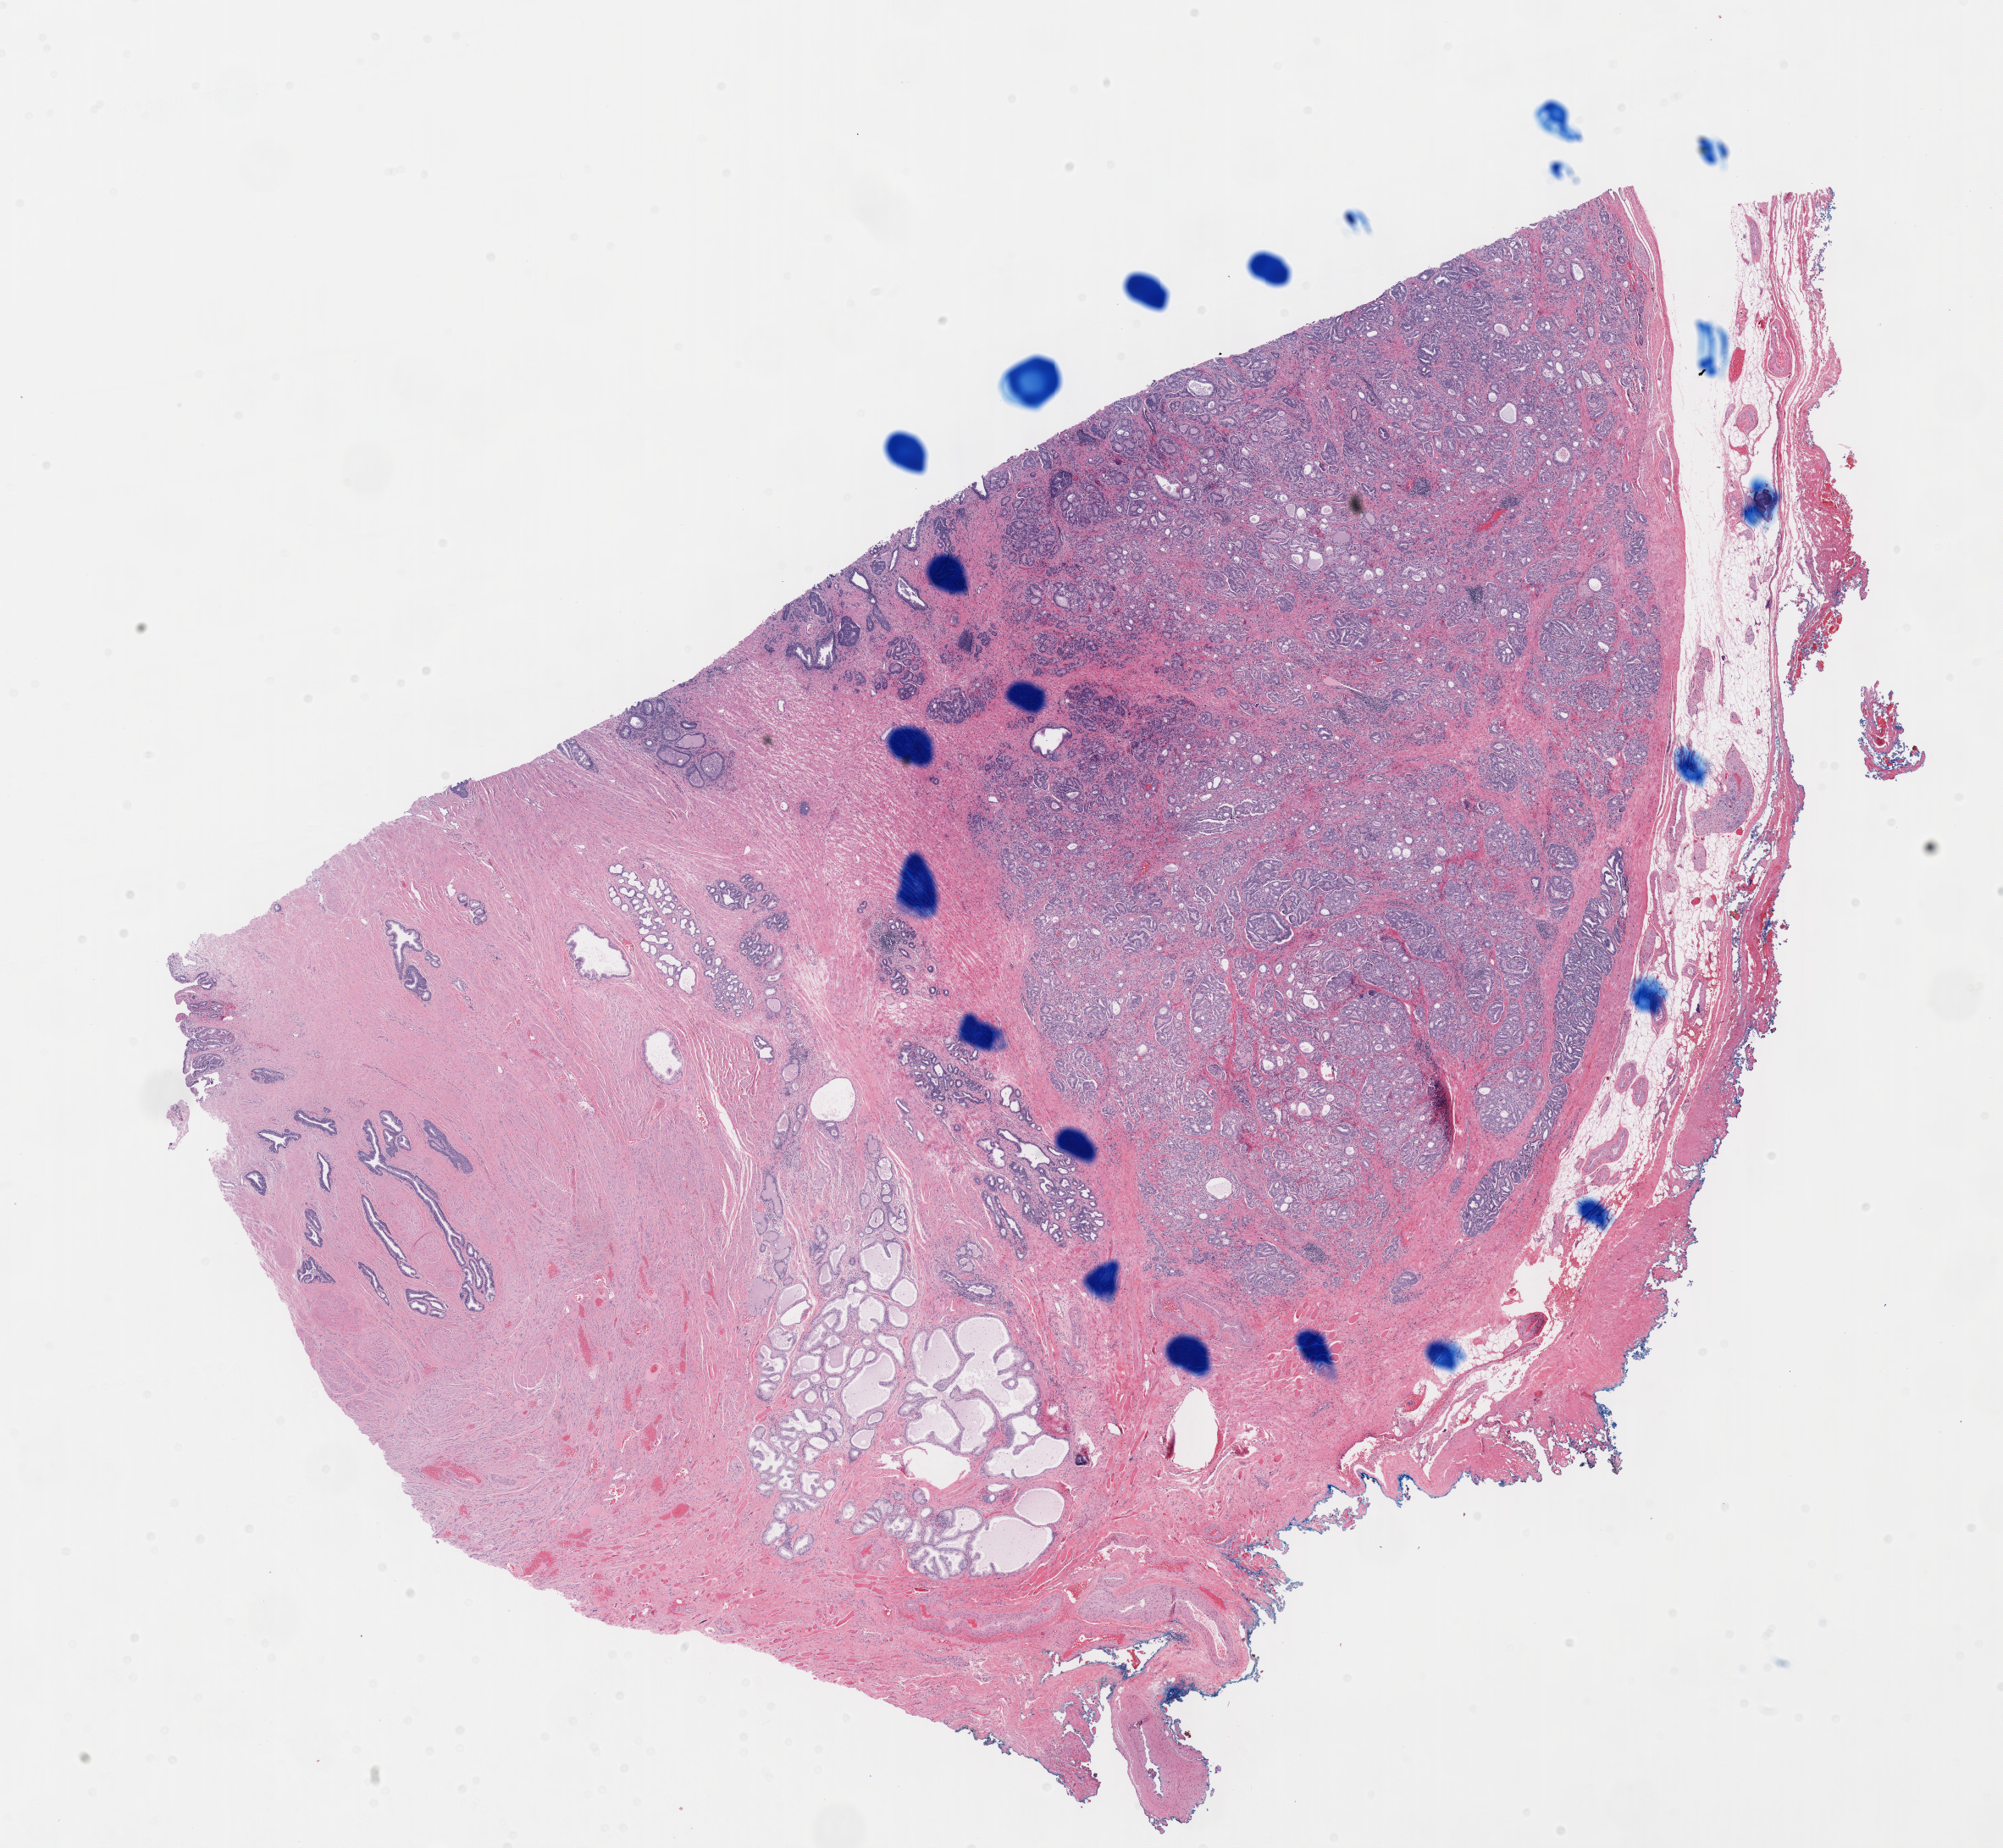
Digitized H&E-stained tissue section (whole slide) — shown as a low-resolution overview of the whole scanned area (about 19.1 x 17.6 mm, slide scanned at 40x). Formalin-fixed paraffin-embedded (FFPE) diagnostic section. Primary tumour sample from the prostate. Male patient; age at initial diagnosis 59 years. Gleason score: 9 (4+5).
• histologic diagnosis: Adenocarcinoma, NOS (prostate gland)